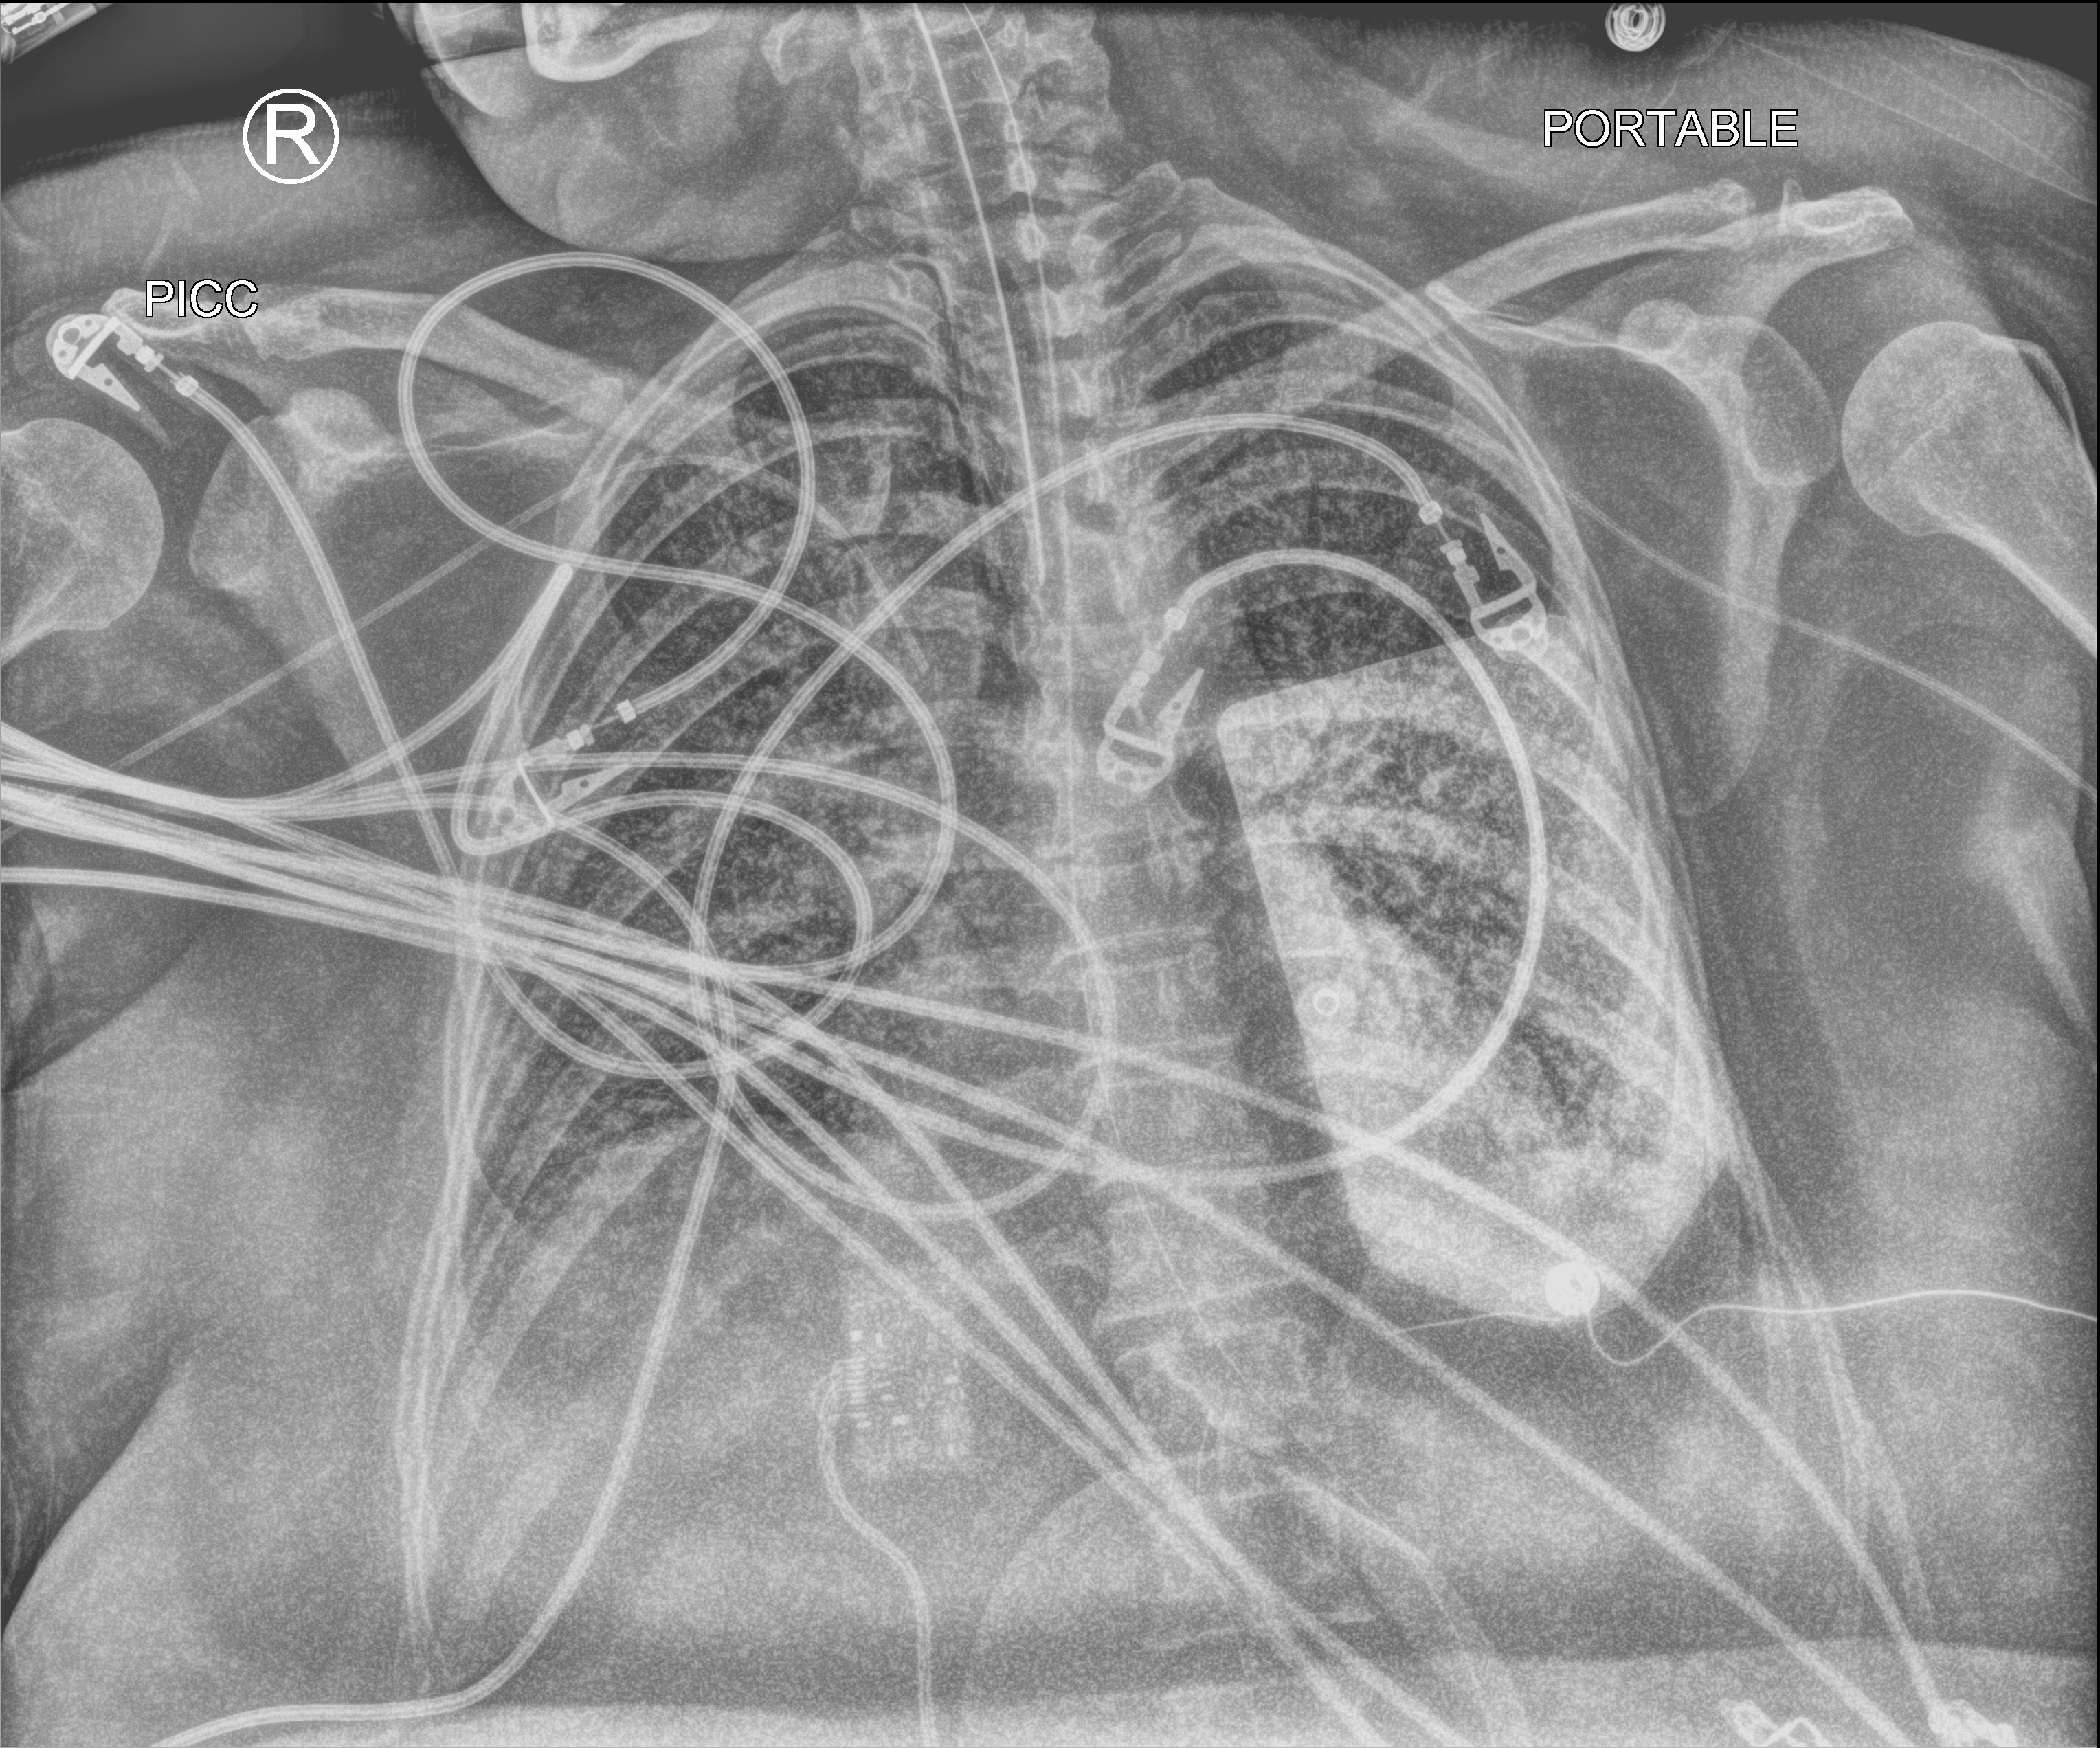
Portable chest radiograph, anteroposterior (AP) projection. Female patient hospitalised with COVID-19, age 18–59 years.
From the hospital-stay record, not from the radiograph (when in the stay this image was taken is not recorded): mechanically ventilated during this hospital stay: yes; diabetes (admission record): no; admitted to intensive care during this hospital stay: yes.